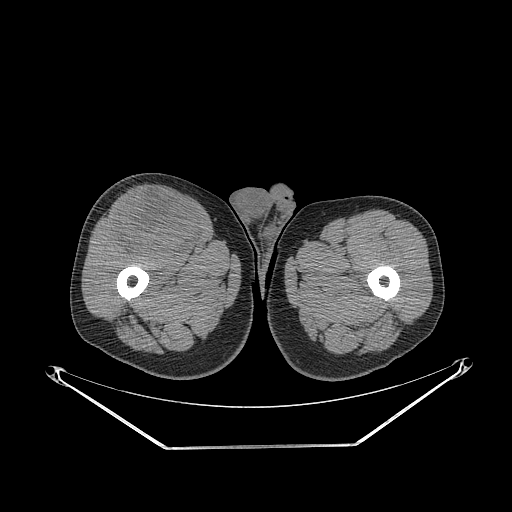
CT of an extremity soft-tissue mass (from a PET/CT study), one axial slice. Position 282 of 311 along the scan axis. Reconstruction kernel STANDARD. 140 kVp. Soft-tissue window (W 400 / L 40 HU). 3.75 mm slice thickness. 512 × 512 image matrix, field of view 500 × 500 mm. Male patient. From the clinical record (not read from this slice): histological type: pleiomorphic leiomyosarcoma; grade: intermediate; site of the primary tumour: right thigh.
Annotated regions visible in this slice (expert contour drawn on MRI and transferred to this co-registered scan by the dataset authors):
- gross tumour volume including surrounding oedema: box from (x=112, y=191) to (x=202, y=259) px
- gross tumour volume (mass): (x=112, y=191)–(x=202, y=259)